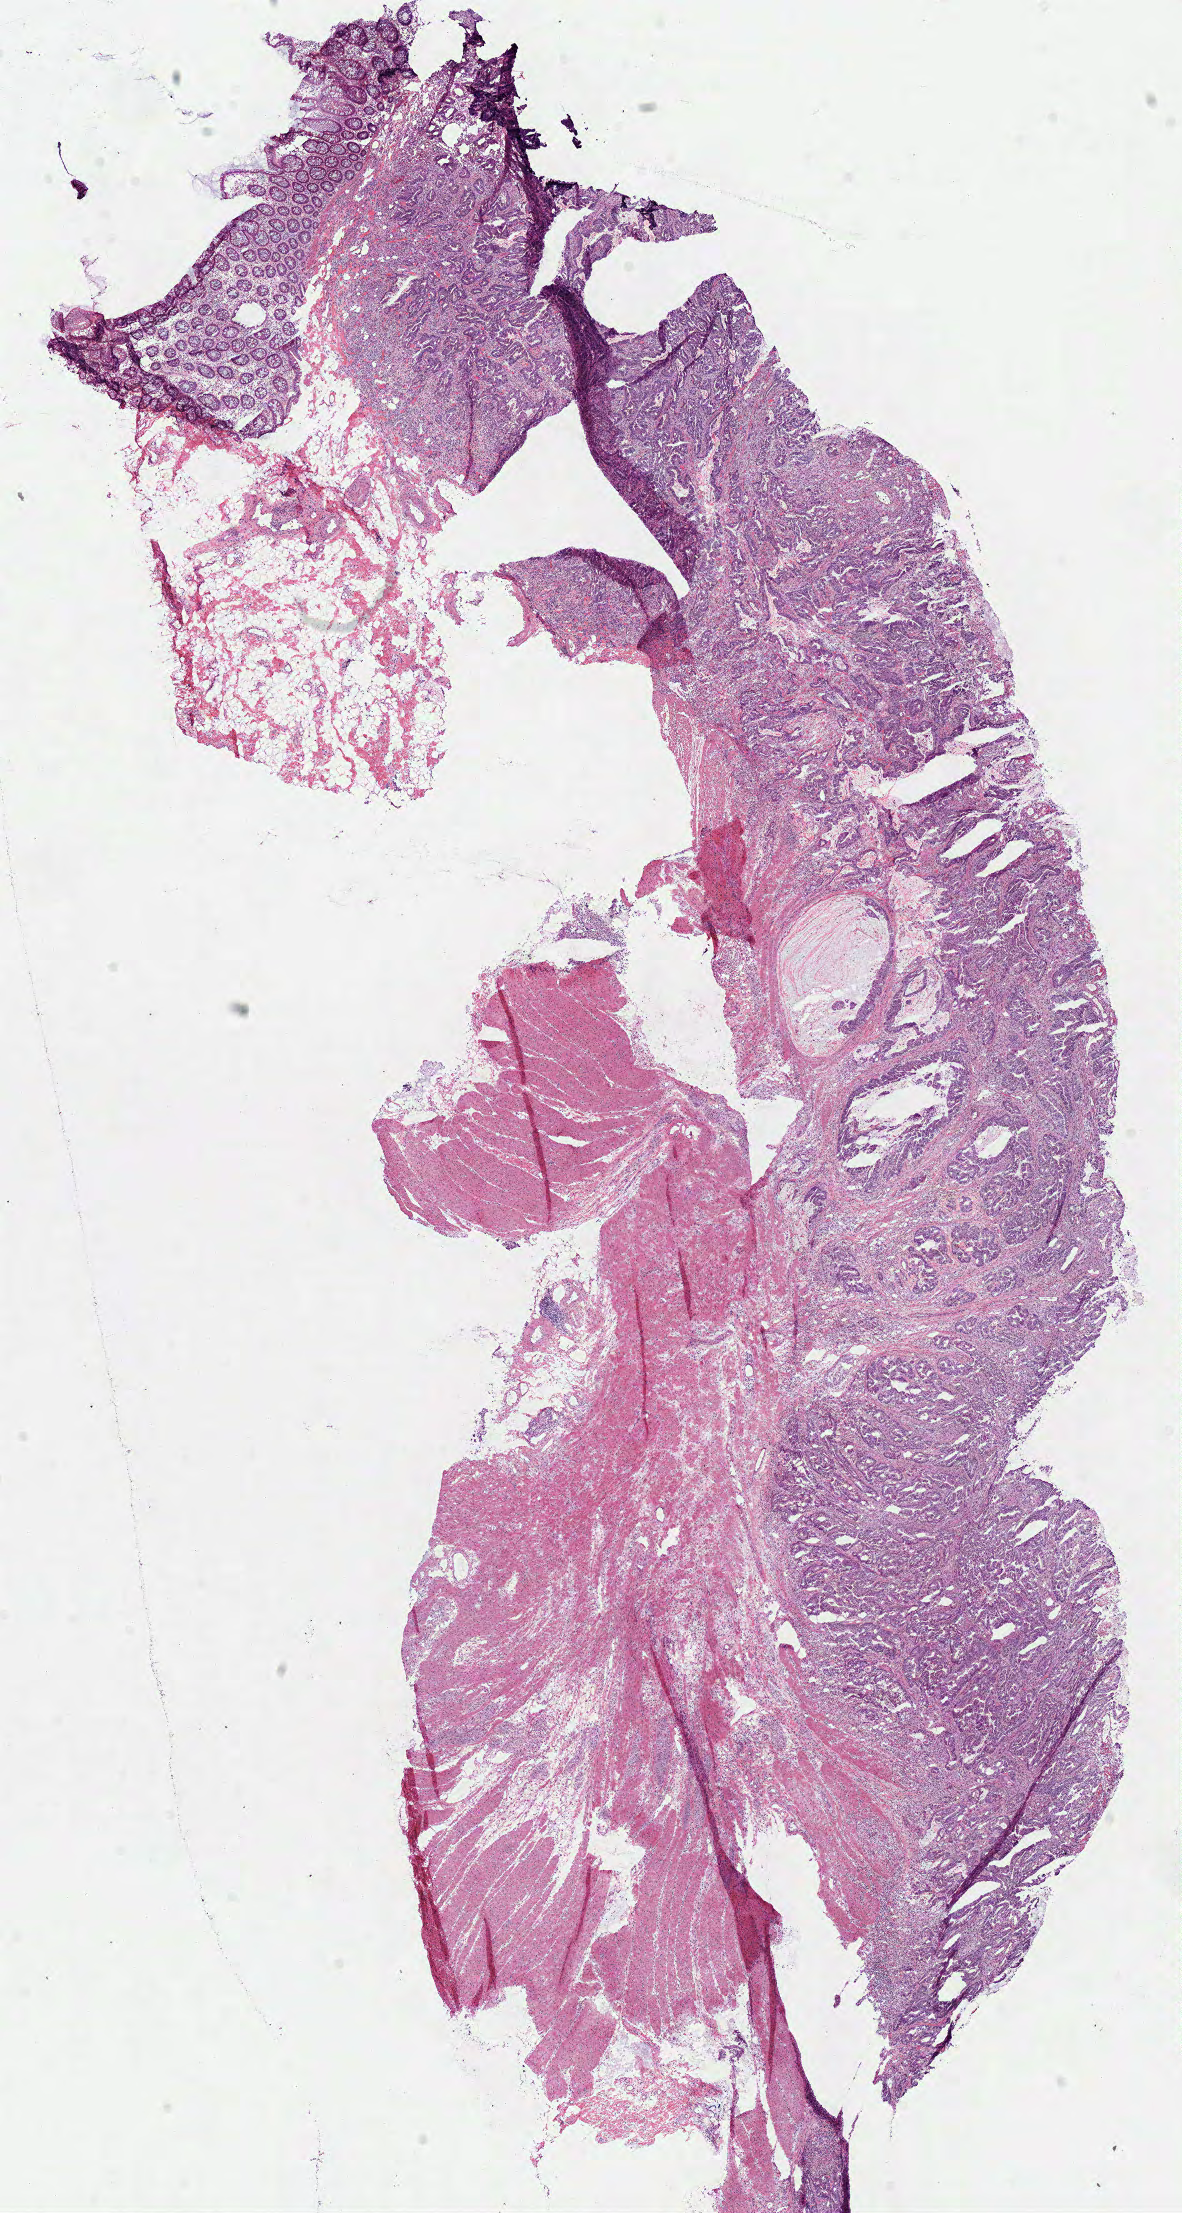
Whole-slide histology image, Hematoxylin and eosin (H&E) stained, a low-resolution overview of the entire scanned area, about 9.3 x 17.4 mm (slide scanned at 40x); frozen section from the bottom of the tissue portion; primary tumour sample from the colon. Patient: female, age at initial diagnosis 84 years. Composition of this section per pathologist review: tumour cells 57%, tumour nuclei 70%, normal cells 8%, stromal cells 30%, necrosis 5%.
Lymph nodes positive (case pathology): 0 of 31 examined. AJCC pathologic stage: IIA (7th edition). Pathologic diagnosis: Adenocarcinoma, NOS (ascending colon).